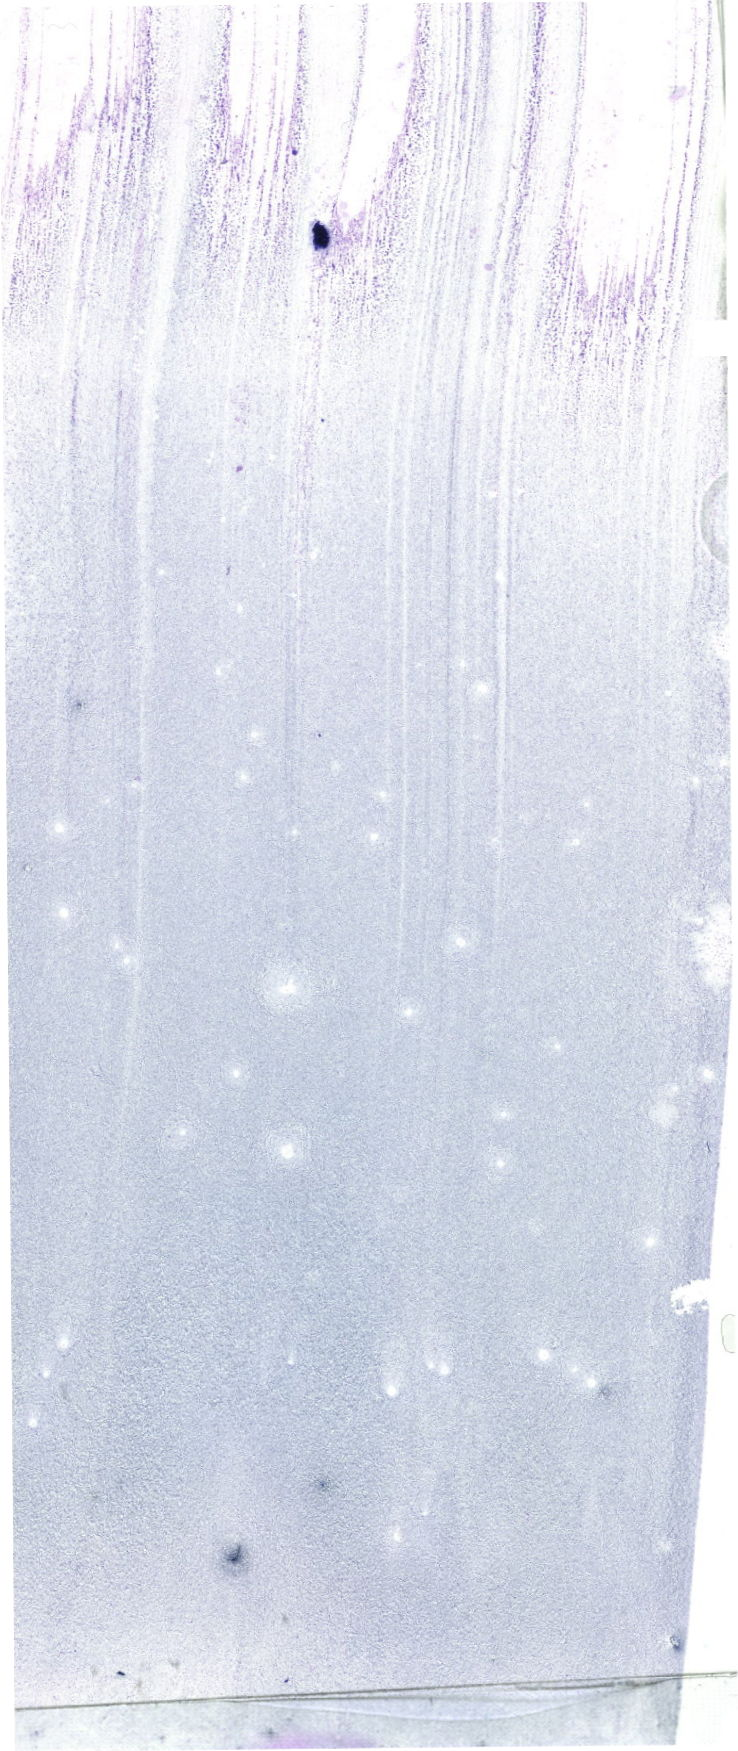
May-Grünwald-Giemsa (MGG)-stained marrow aspirate smear (whole slide), whole scanned area (about 20.9 x 49.6 mm) shown as a low-resolution overview. Male patient.
* diagnosis: B Acute Lymphoblastic Leukemia